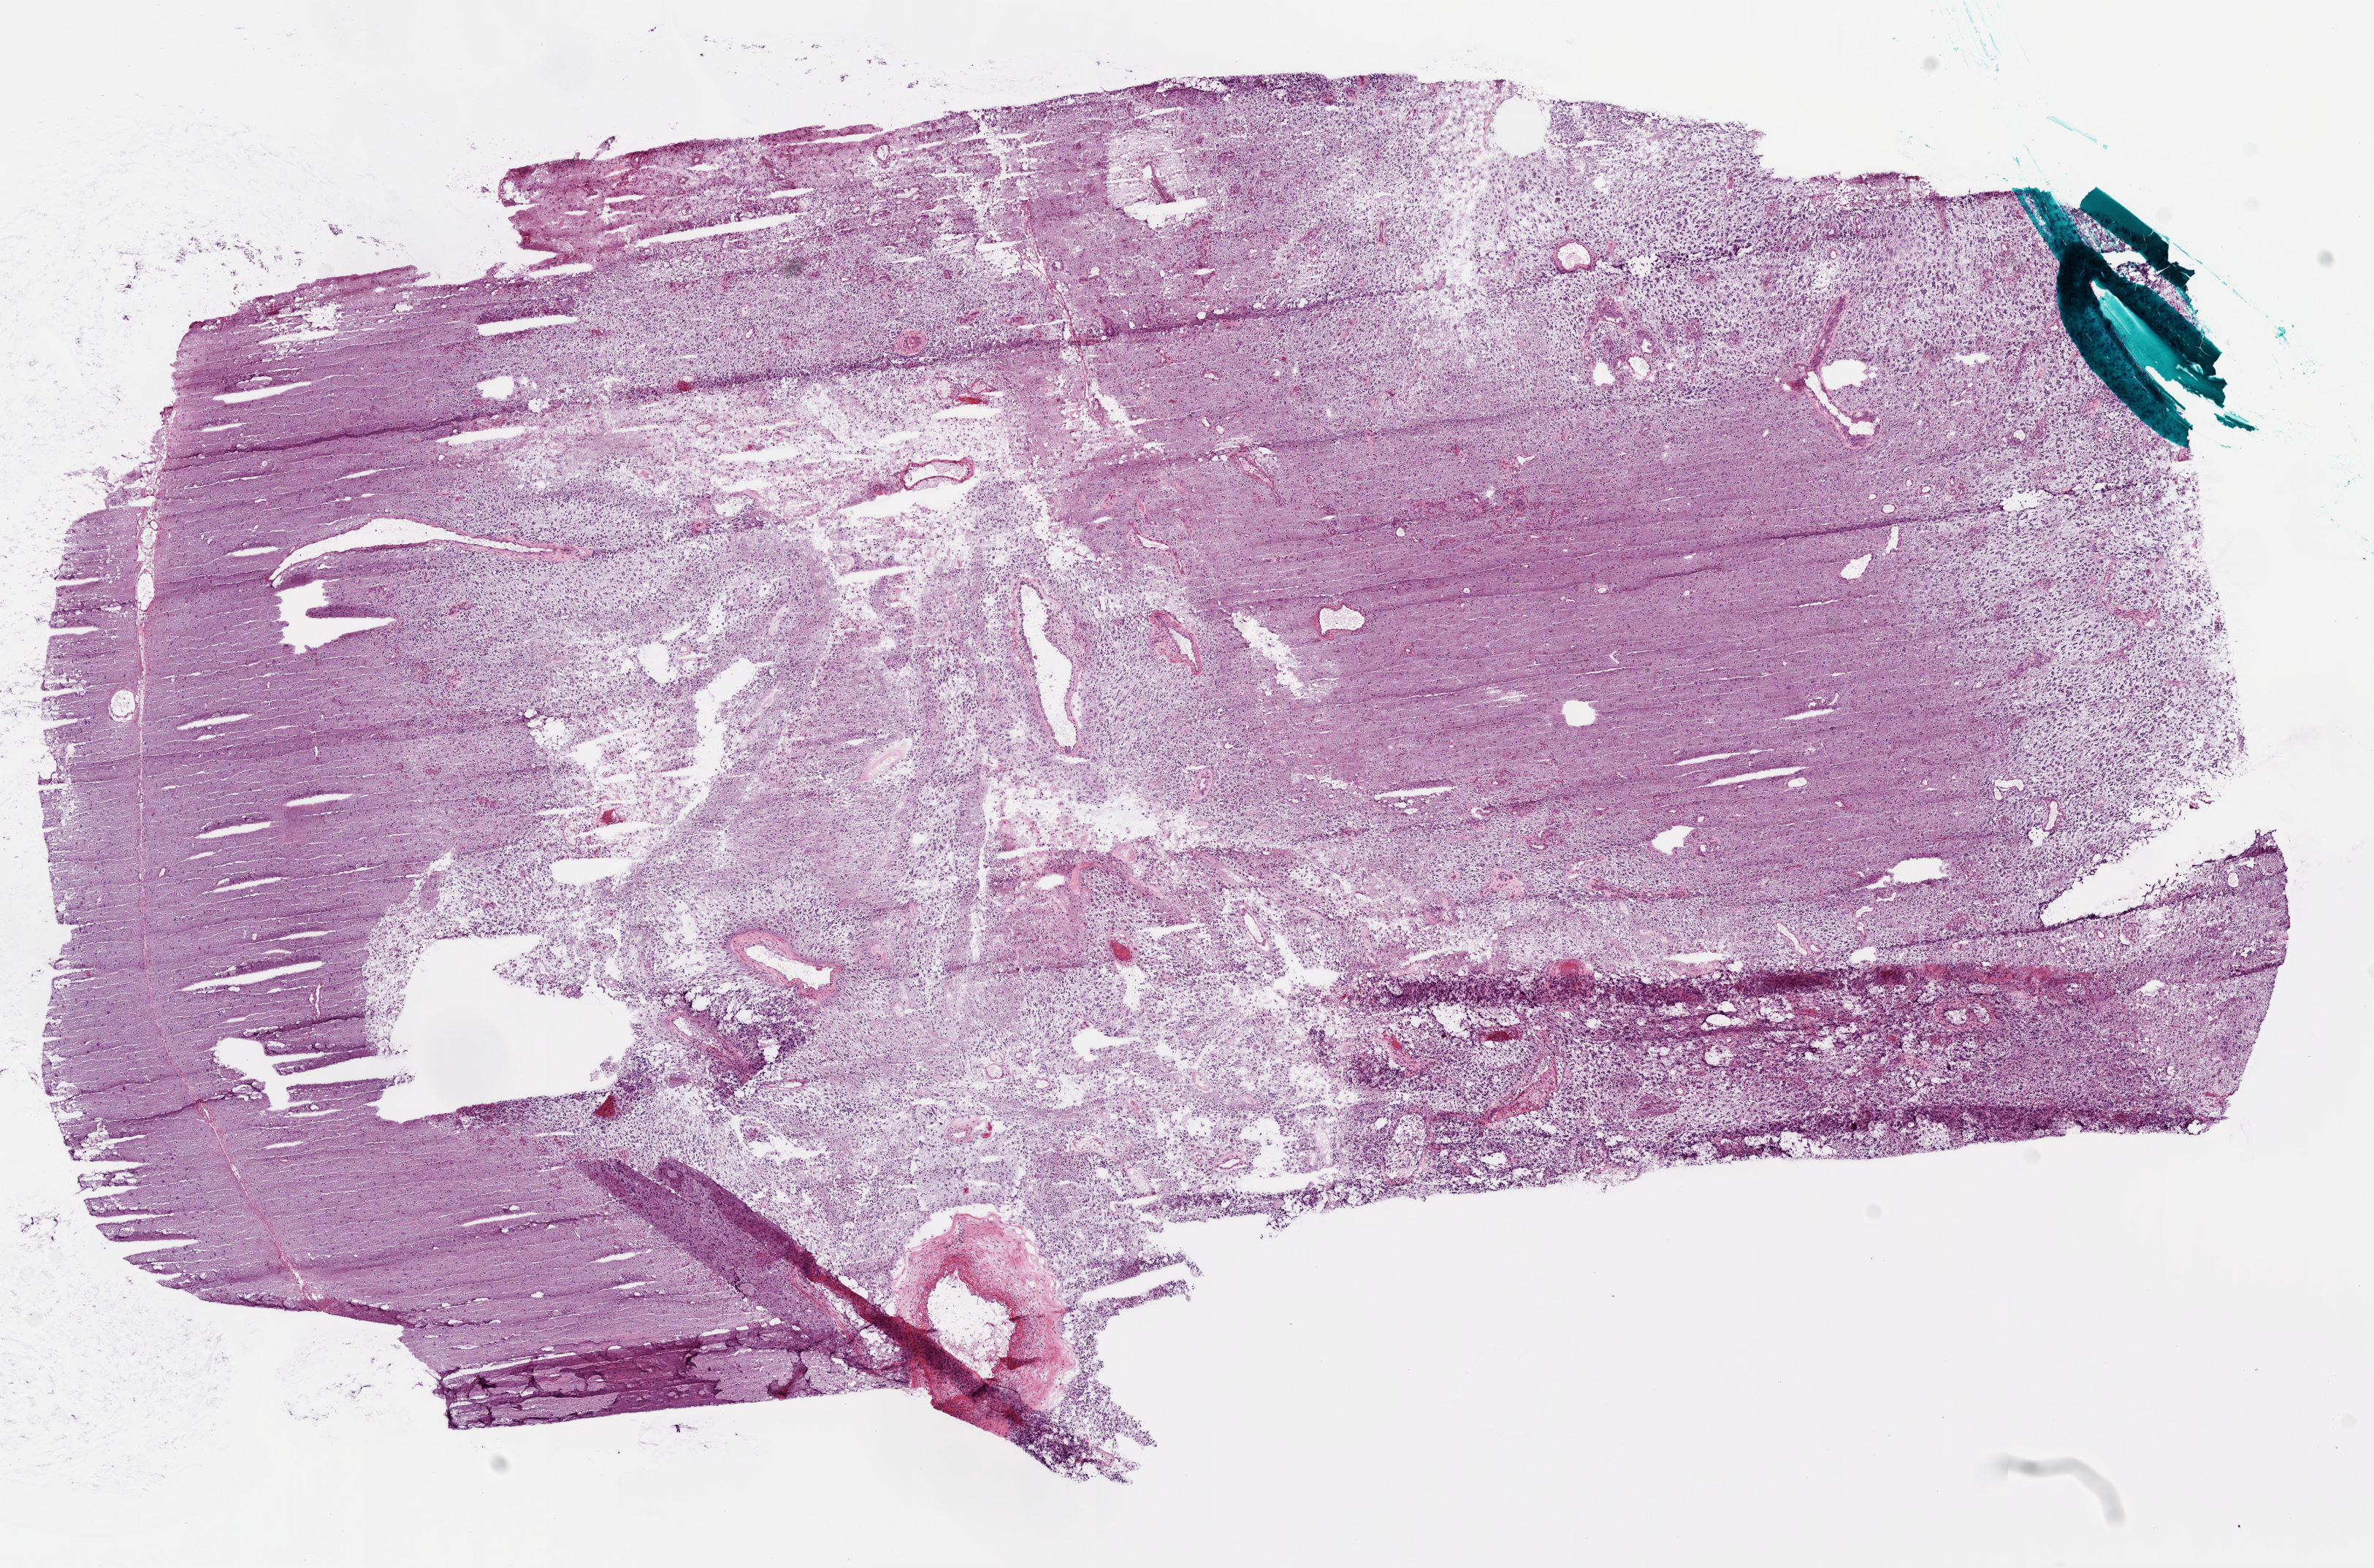
H&E whole-slide image, a low-resolution overview of the entire scanned area, about 13.0 x 8.6 mm (acquisition: 20x scan). Frozen section from the bottom of the tissue portion. Brain, primary tumour sample. Male patient; age at initial diagnosis 61 years. Pathologist review of this section (percent, as recorded): tumour cells 50%, tumour nuclei 100%, normal cells 30%, stromal cells 20%, necrosis 0%.
• diagnosis: Glioblastoma